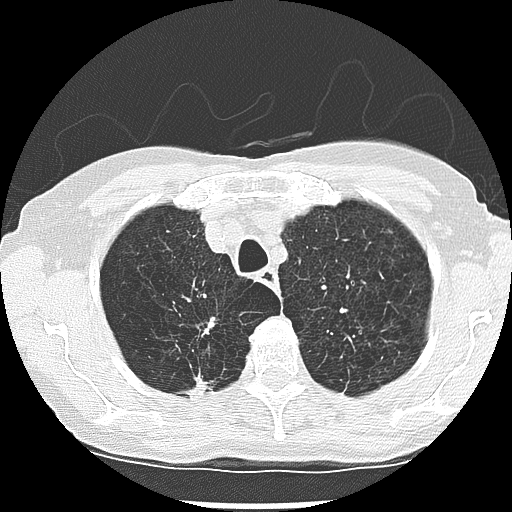
Low-dose screening chest CT, one axial slice; position 223 of 265 along the scan axis; 120 kVp; lung window (W 1500 / L -600 HU); 2.5 mm slice thickness; 512 × 512 image matrix, field of view 300 × 300 mm.
Outlined on this slice (outlined manually by an expert reader):
- lesion 1 (nodule, upper lobe of right lung): bounding box (x1, y1, x2, y2) in pixels: (188, 375, 208, 396)